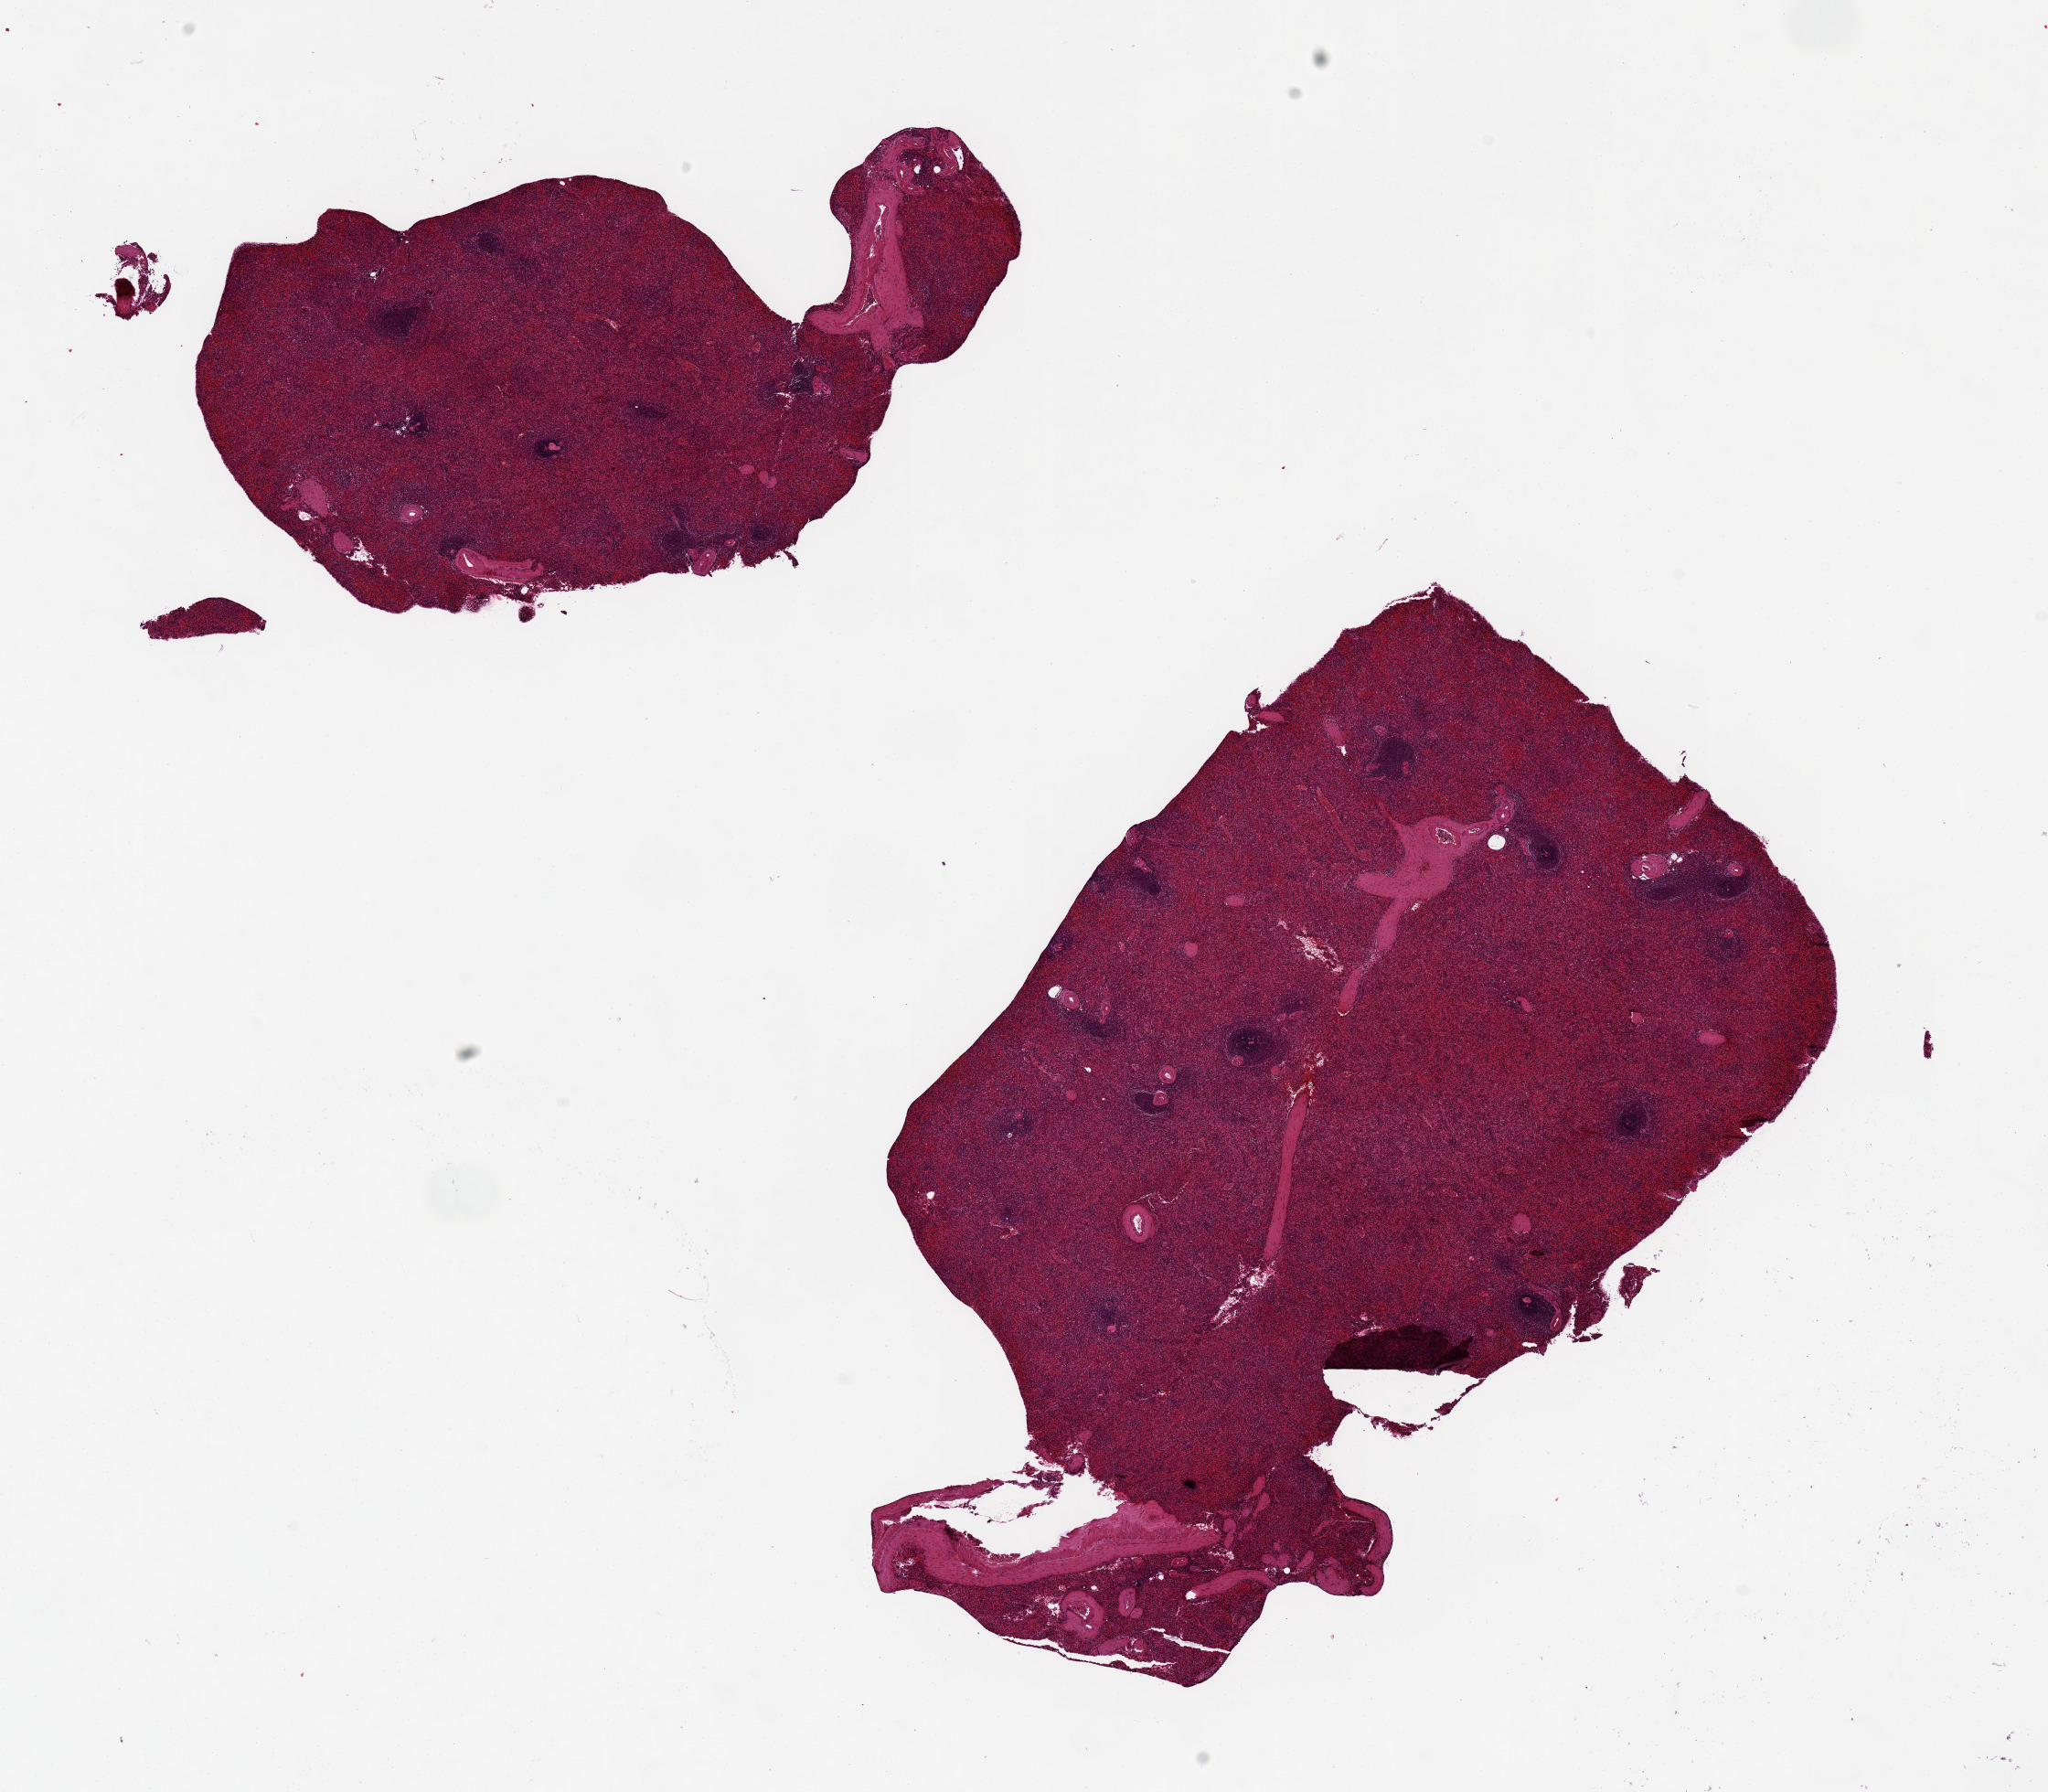
Hematoxylin and eosin (H&E) whole-slide image — whole scanned area (about 17.7 x 15.5 mm, acquisition: 20x scan) shown as a low-resolution overview; PAXgene-fixed, paraffin-embedded tissue; sampled site (target tissue): spleen; tissue donor sample. Male donor.
Reviewer comment on this tissue sample: 2 aliquots. Marked congestion of red pulp.